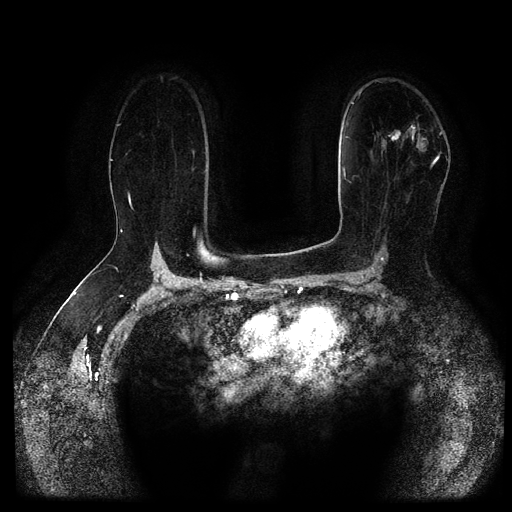
Breast MRI (dynamic contrast-enhanced, multi-phase), one axial slice; slice 68 of 116 in the series (ordered by position); dynamic contrast-enhanced series, time point 2 of 5 at this slice position (early post-contrast); 1.5 T; TE 2.6 ms, TR 5.3 ms; 2 mm slice thickness; 512 × 512 image matrix, field of view 360 × 360 mm. Female patient, age 67 years.
Annotated regions visible in this slice (semi-automatic segmentation, software-assisted and operator-edited):
- breast lesion (labelled 'tumour' in the annotation; benign lesions carry a separate 'benign' label): bounding box <388,124,416,147> (left, top, right, bottom; pixels)